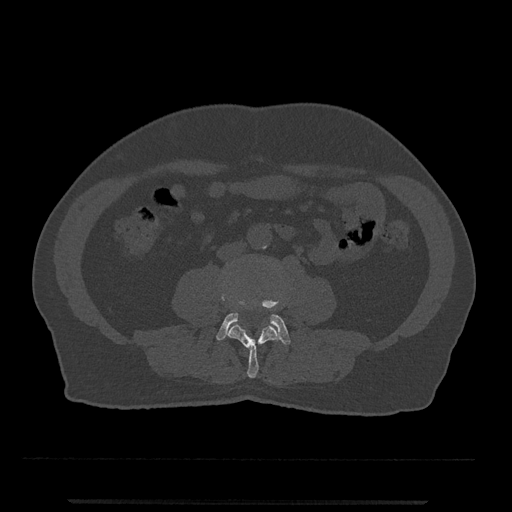
CT including the spine, one axial slice. Slice 171 of 797 in the series (ordered by position). Reconstruction kernel Br40s/3. 120 kVp. Bone window (W 1800 / L 400 HU). 0.5 mm slice thickness. 512 × 512 image matrix, field of view 419 × 419 mm. Patient: male, 63 years. From the clinical record (not read from this slice): primary cancer: prostate.
Annotated regions visible in this slice (semi-automatic segmentation, software-assisted and operator-edited):
- L3 vertebra: bounding box <220,293,281,378> (left, top, right, bottom; pixels)
- L4 vertebra: <216,300,291,345>